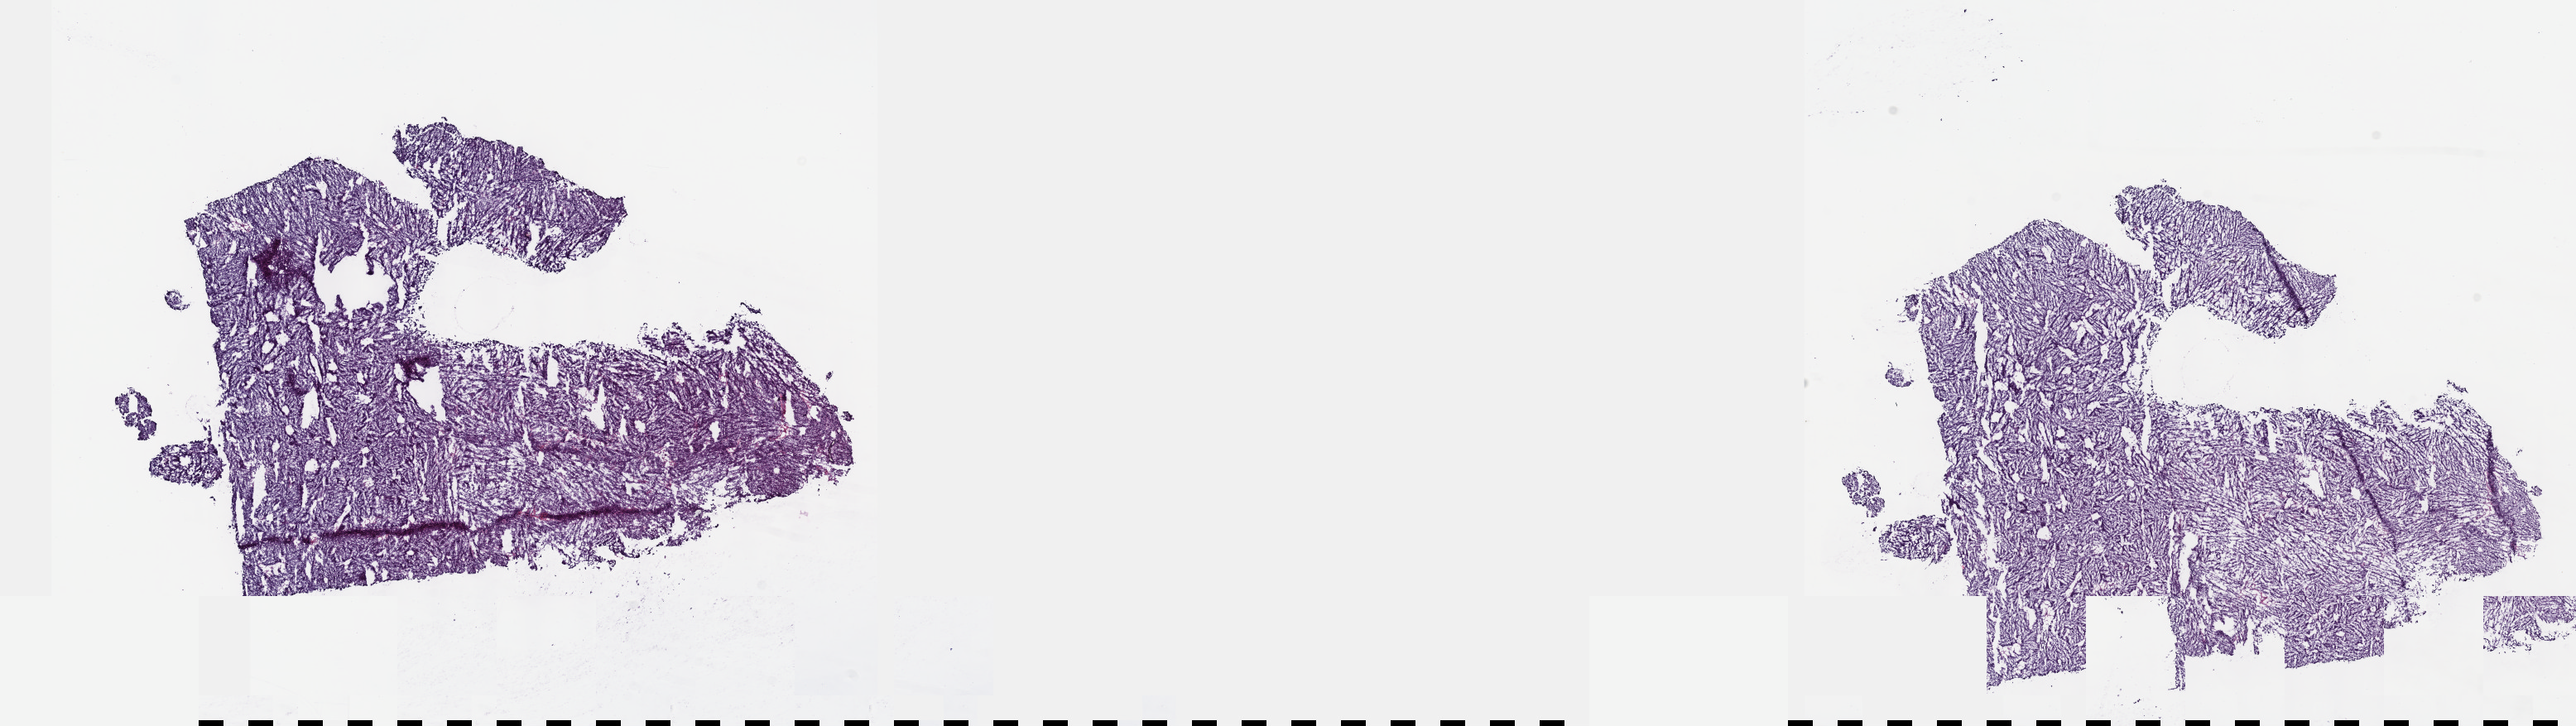
Whole-slide histology image, Hematoxylin and eosin (H&E) stained — a low-resolution overview of the entire scanned area, about 25.1 x 7.1 mm (slide scanned at 40x), frozen section from the top of the tissue portion, sample: primary tumour, liver. Male patient; age at initial diagnosis 49 years. Histologic grade: G1 (well differentiated). Pathologist review of this section (percent, as recorded): tumour cells 100%, tumour nuclei 95%, normal cells 0%, stromal cells 0%, necrosis 0%. Inflammatory infiltration, as recorded: lymphocyte infiltration 0%, monocyte infiltration 0%, neutrophil infiltration 0%.
AJCC pathologic stage: IIIA. Histologic diagnosis: Hepatocellular carcinoma, NOS.